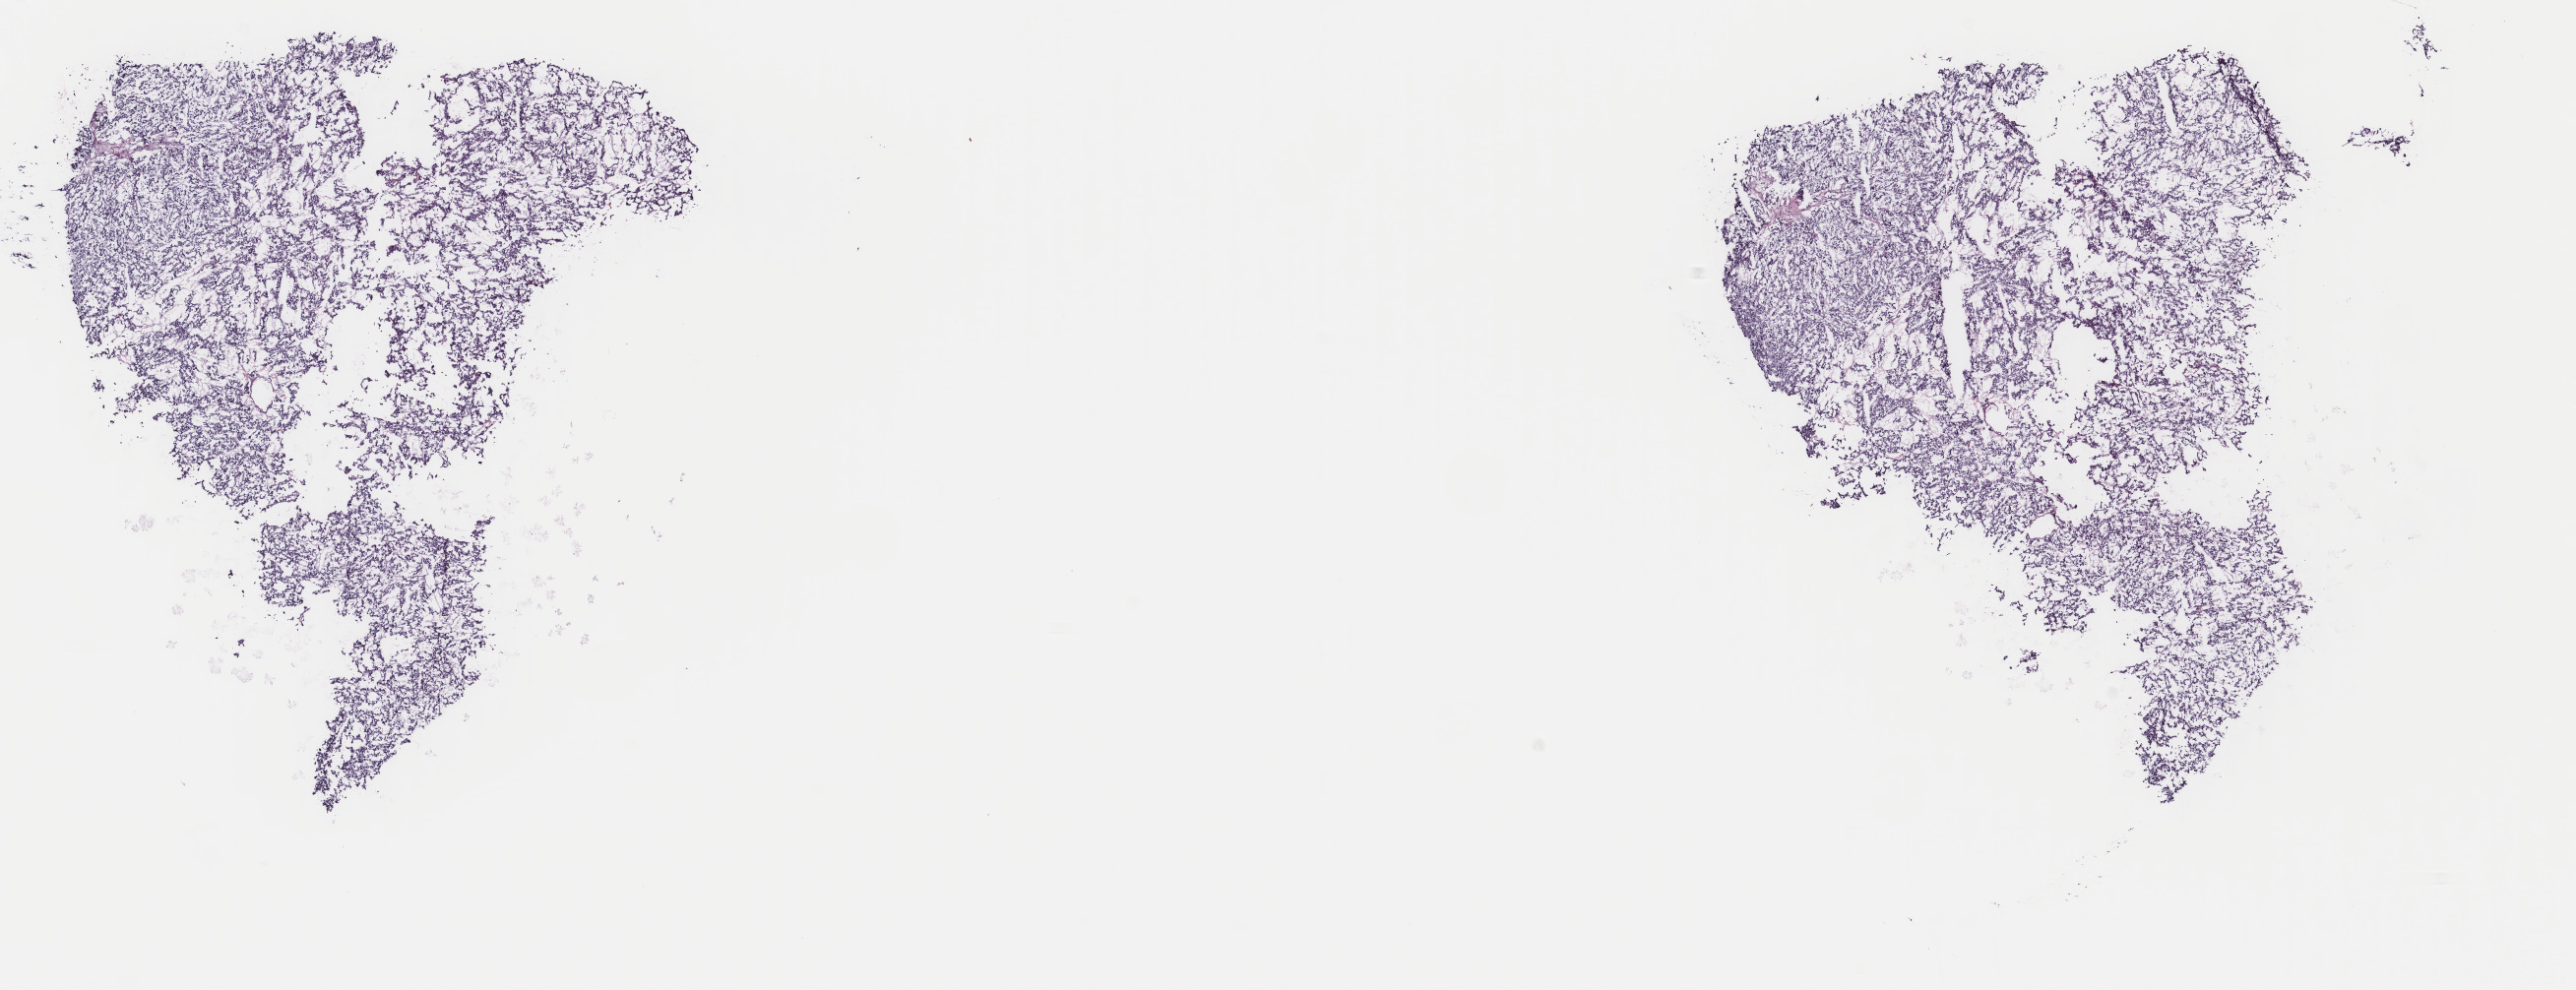
Hematoxylin and eosin (H&E) stained whole-slide image, shown as a low-resolution overview of the whole scanned area (about 20.8 x 8.0 mm, slide scanned at 40x); frozen section; sample: primary tumour, adrenal gland. Male, age 31 years at initial diagnosis. Slide review estimates, as recorded: tumour cells 99%, tumour nuclei 99%, normal cells 0%, stromal cells 1%, necrosis 0%. Inflammatory infiltration, as recorded: lymphocyte infiltration 0%, monocyte infiltration 0%, neutrophil infiltration 0%.
Histologic diagnosis: Medullary carcinoma, NOS (thyroid gland).